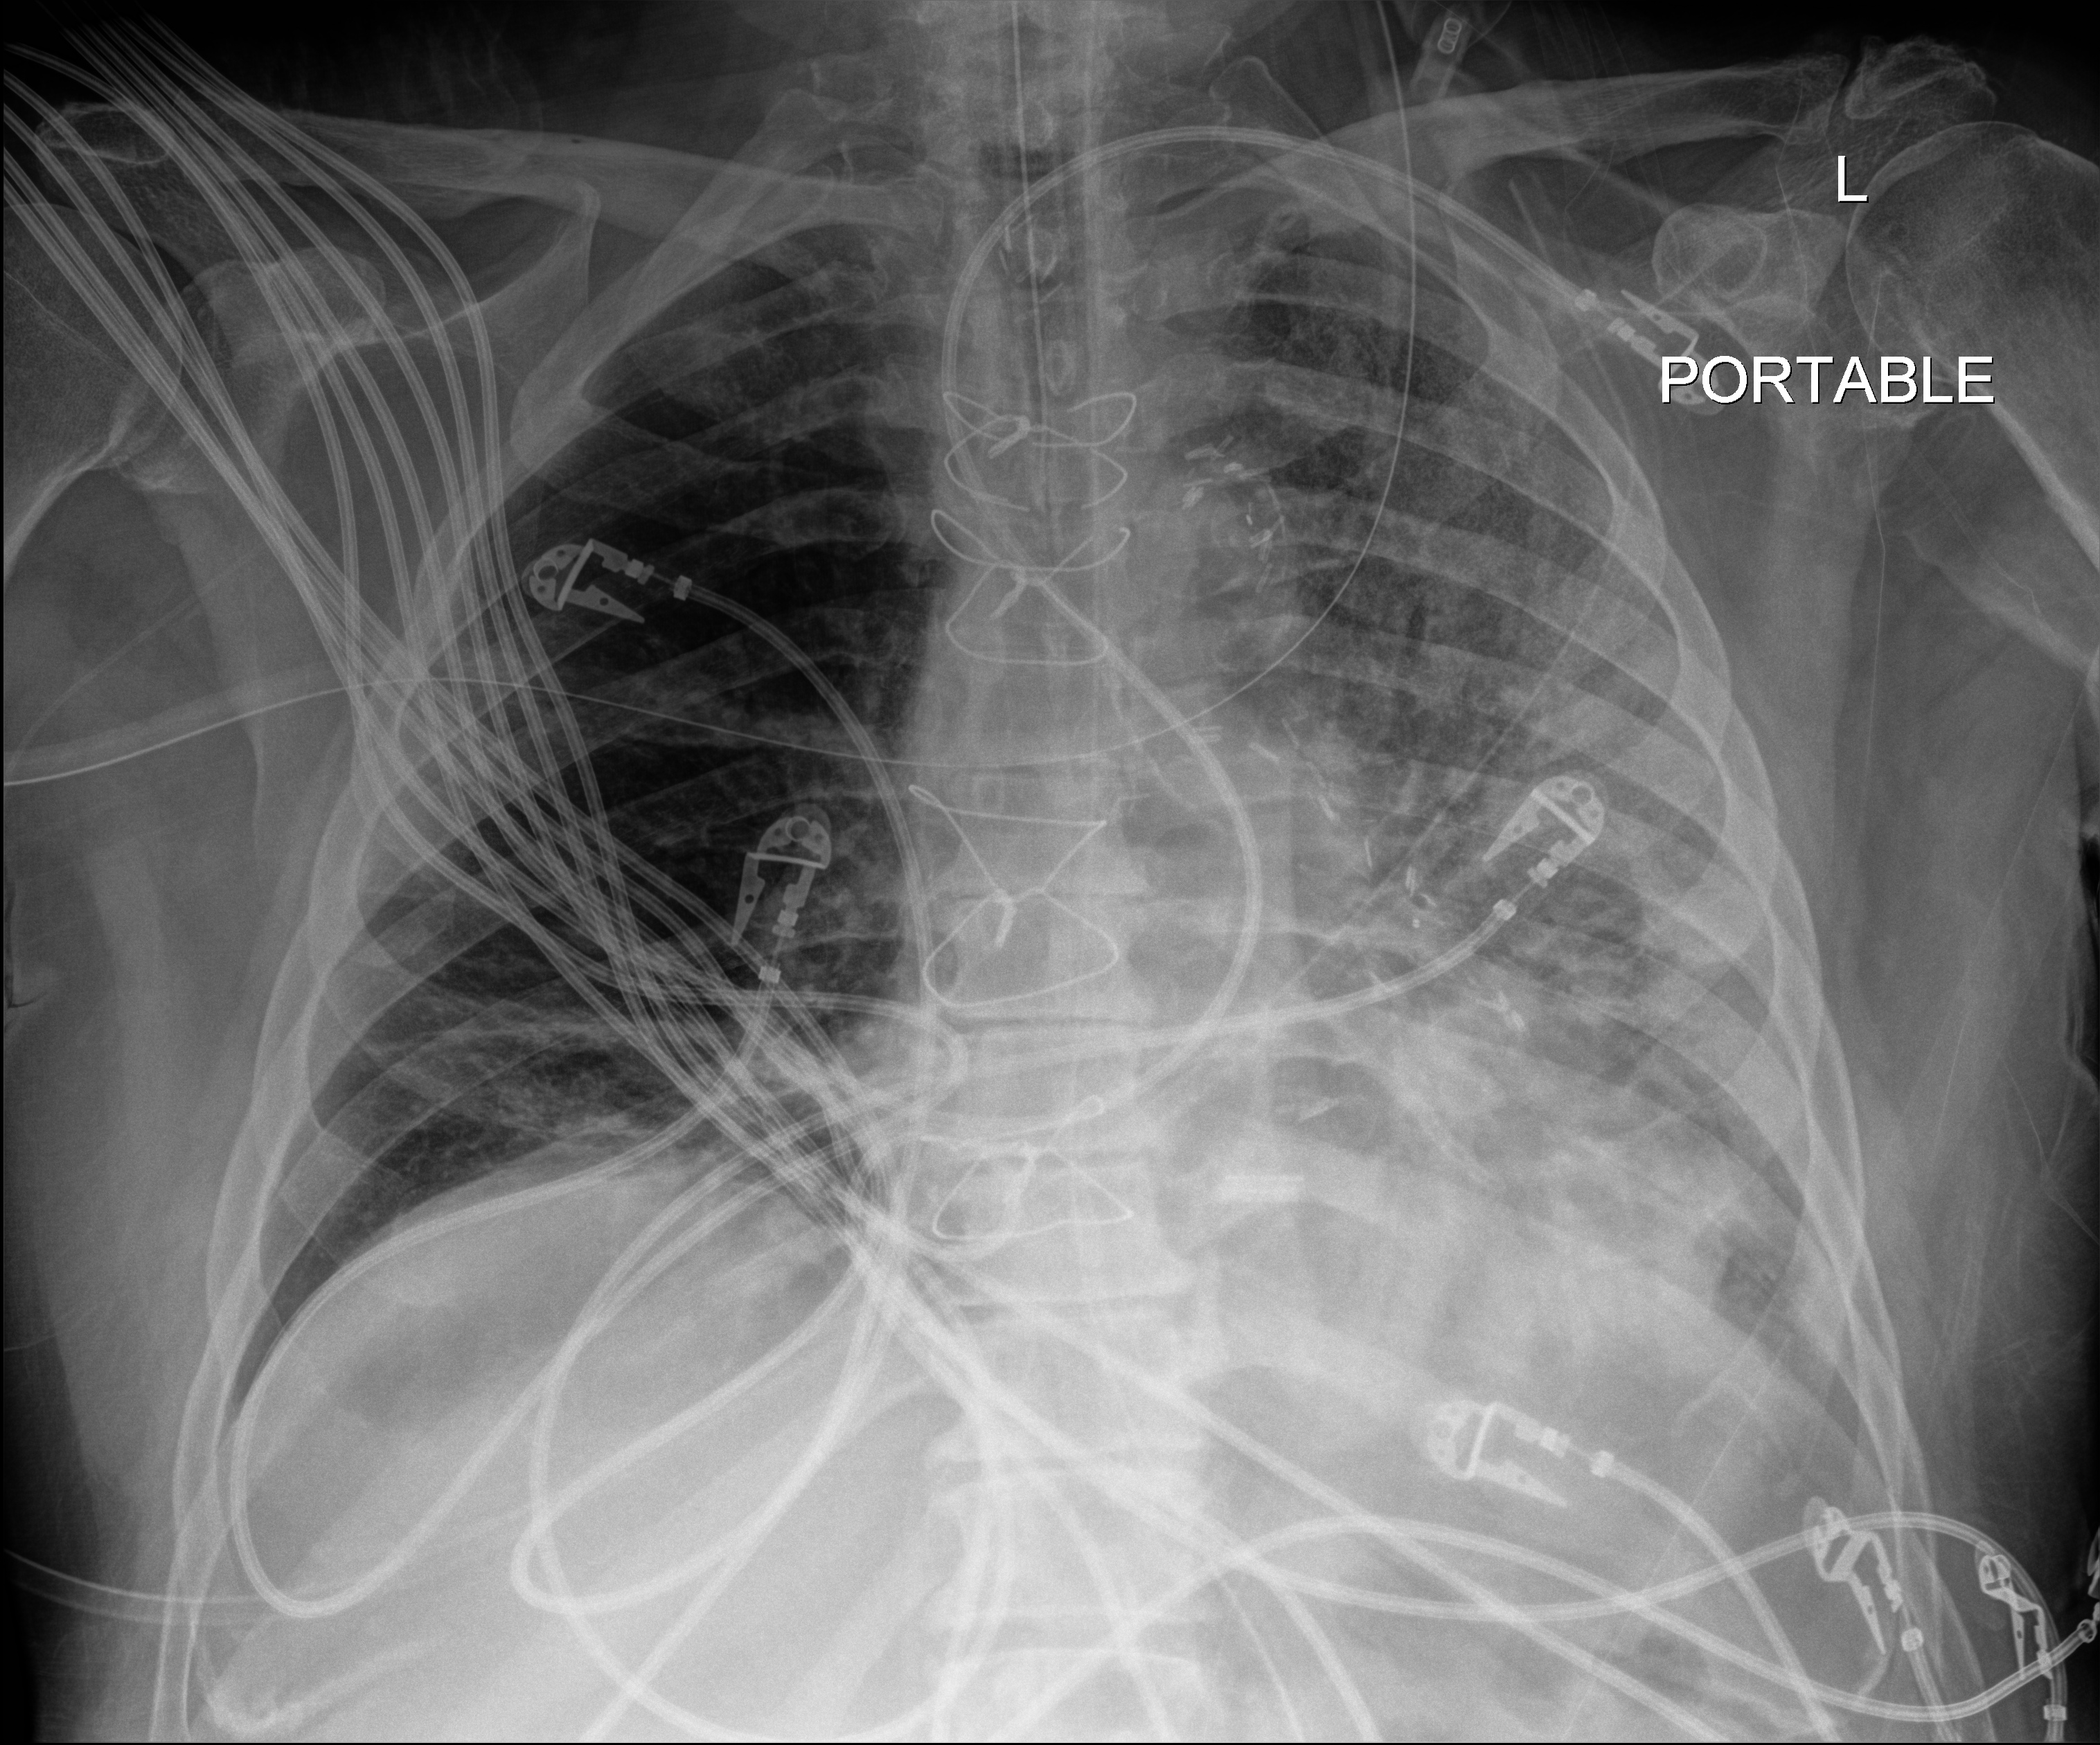
Bedside chest radiograph (digital radiography); anteroposterior (AP) projection. Patient hospitalised with COVID-19; male, aged 60–74 years.
Admission-level facts for this patient (not findings on this image; timing relative to this image not recorded):
- admitted to intensive care during this hospital stay: yes
- hypertension (admission record): yes